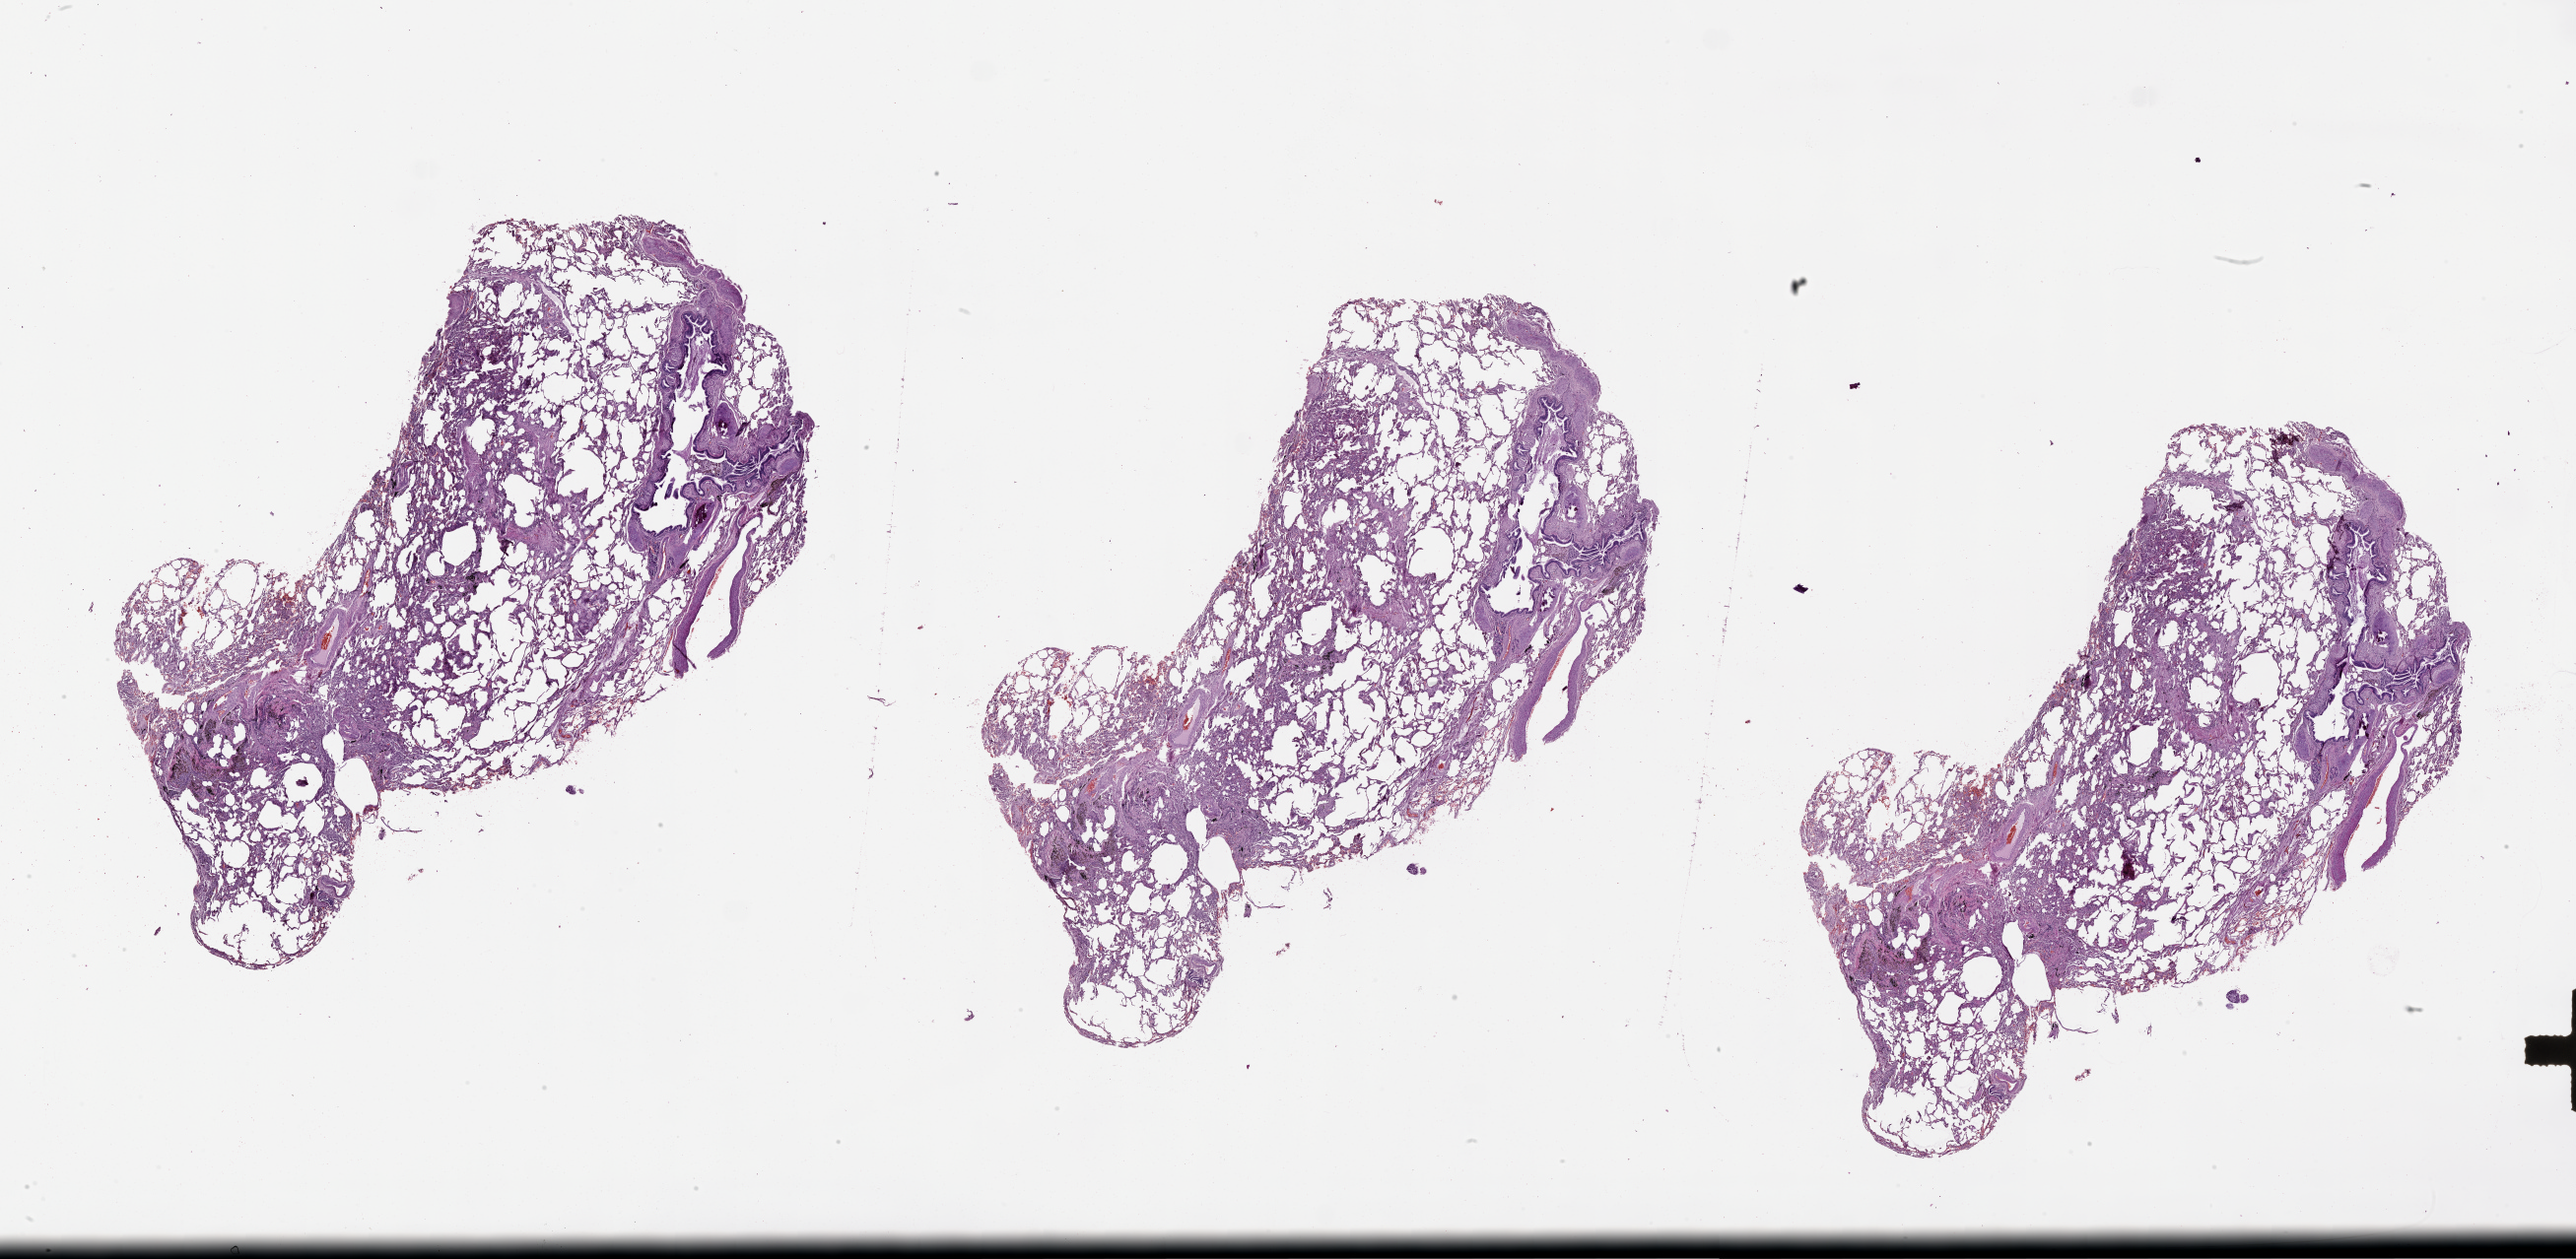
Digitized H&E-stained tissue section (whole slide) — low-resolution overview of the scanned area, about 42.1 x 20.6 mm (slide scanned at 20x). Lung, normal (non-tumour) tissue. Female, 62 y/o.
* this section: normal (non-tumour) tissue from the same patient
* patient diagnosis (cohort enrolment): squamous cell carcinoma (lung)